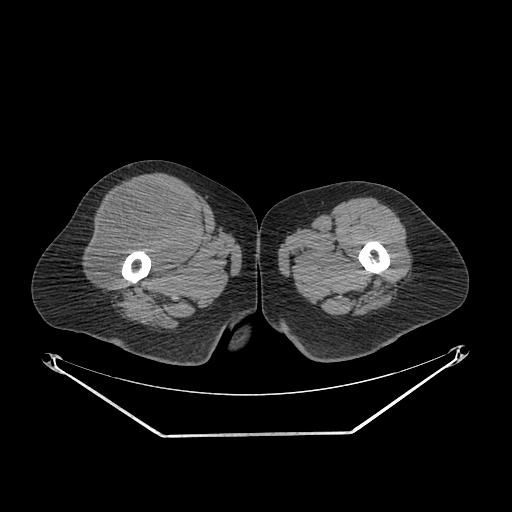
CT of an extremity soft-tissue mass (from a PET/CT study), one axial slice. Position 260 of 311 along the scan axis. Soft-tissue window (W 400 / L 40 HU). 3.75 mm slice thickness. 512 × 512 image matrix, field of view 500 × 500 mm. Female patient. From the clinical record (not read from this slice): histological type: pleiomorphic undifferentiated sarcoma; grade: high; site of the primary tumour: right quadricep.
Annotated regions visible in this slice (expert contour drawn on MRI and transferred to this co-registered scan by the dataset authors):
- tumour plus oedema (research contour): bounding box <91,185,197,284> (left, top, right, bottom; pixels)
- tumour (research contour): <91,185,197,284>